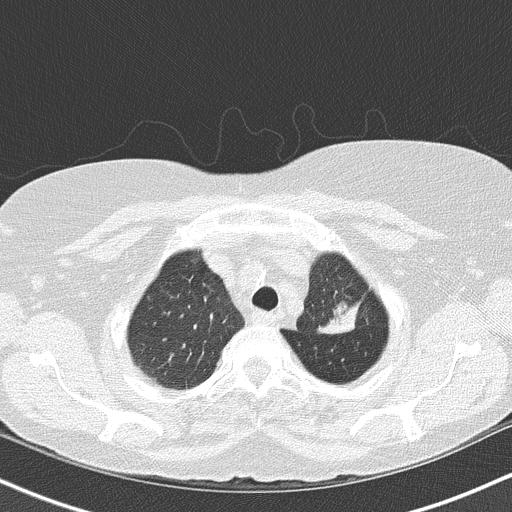
Low-dose screening chest CT, one axial slice; position 127 of 147 along the scan axis; reconstruction kernel B50f; lung window (W 1500 / L -600 HU); 2 mm slice thickness; 512 × 512 image matrix, field of view 320 × 320 mm.
Outlined on this slice (manually delineated by an expert):
- lesion 1 (tumor, upper lobe of left lung): bounding box (x1, y1, x2, y2) in pixels: (320, 303, 358, 334)